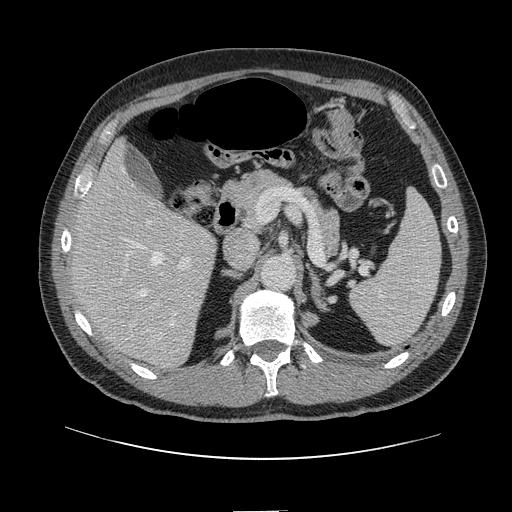
Contrast-enhanced abdominal CT, one axial slice; position 75 of 161 along the scan axis; 120 kVp; intravenous contrast given; soft-tissue window (W 400 / L 40 HU); 2.5 mm slice thickness; 512 × 512 image matrix, field of view 412 × 412 mm. Male patient, age 66 years. From the clinical record (not read from this slice): diagnosis: colorectal cancer liver metastases, imaged before liver resection; multiple liver metastases: no; largest metastasis: 3.5 cm; chemotherapy before resection: yes.
Structures marked on this image (expert manual segmentation):
- hepatic veins: bounding box [x1, y1, x2, y2] px = [121, 167, 173, 326]
- liver: [75, 144, 215, 367]
- planned liver remnant (the part of the liver to remain after resection): [75, 144, 198, 293]
- portal vein (with intrahepatic branches): [122, 220, 191, 313]